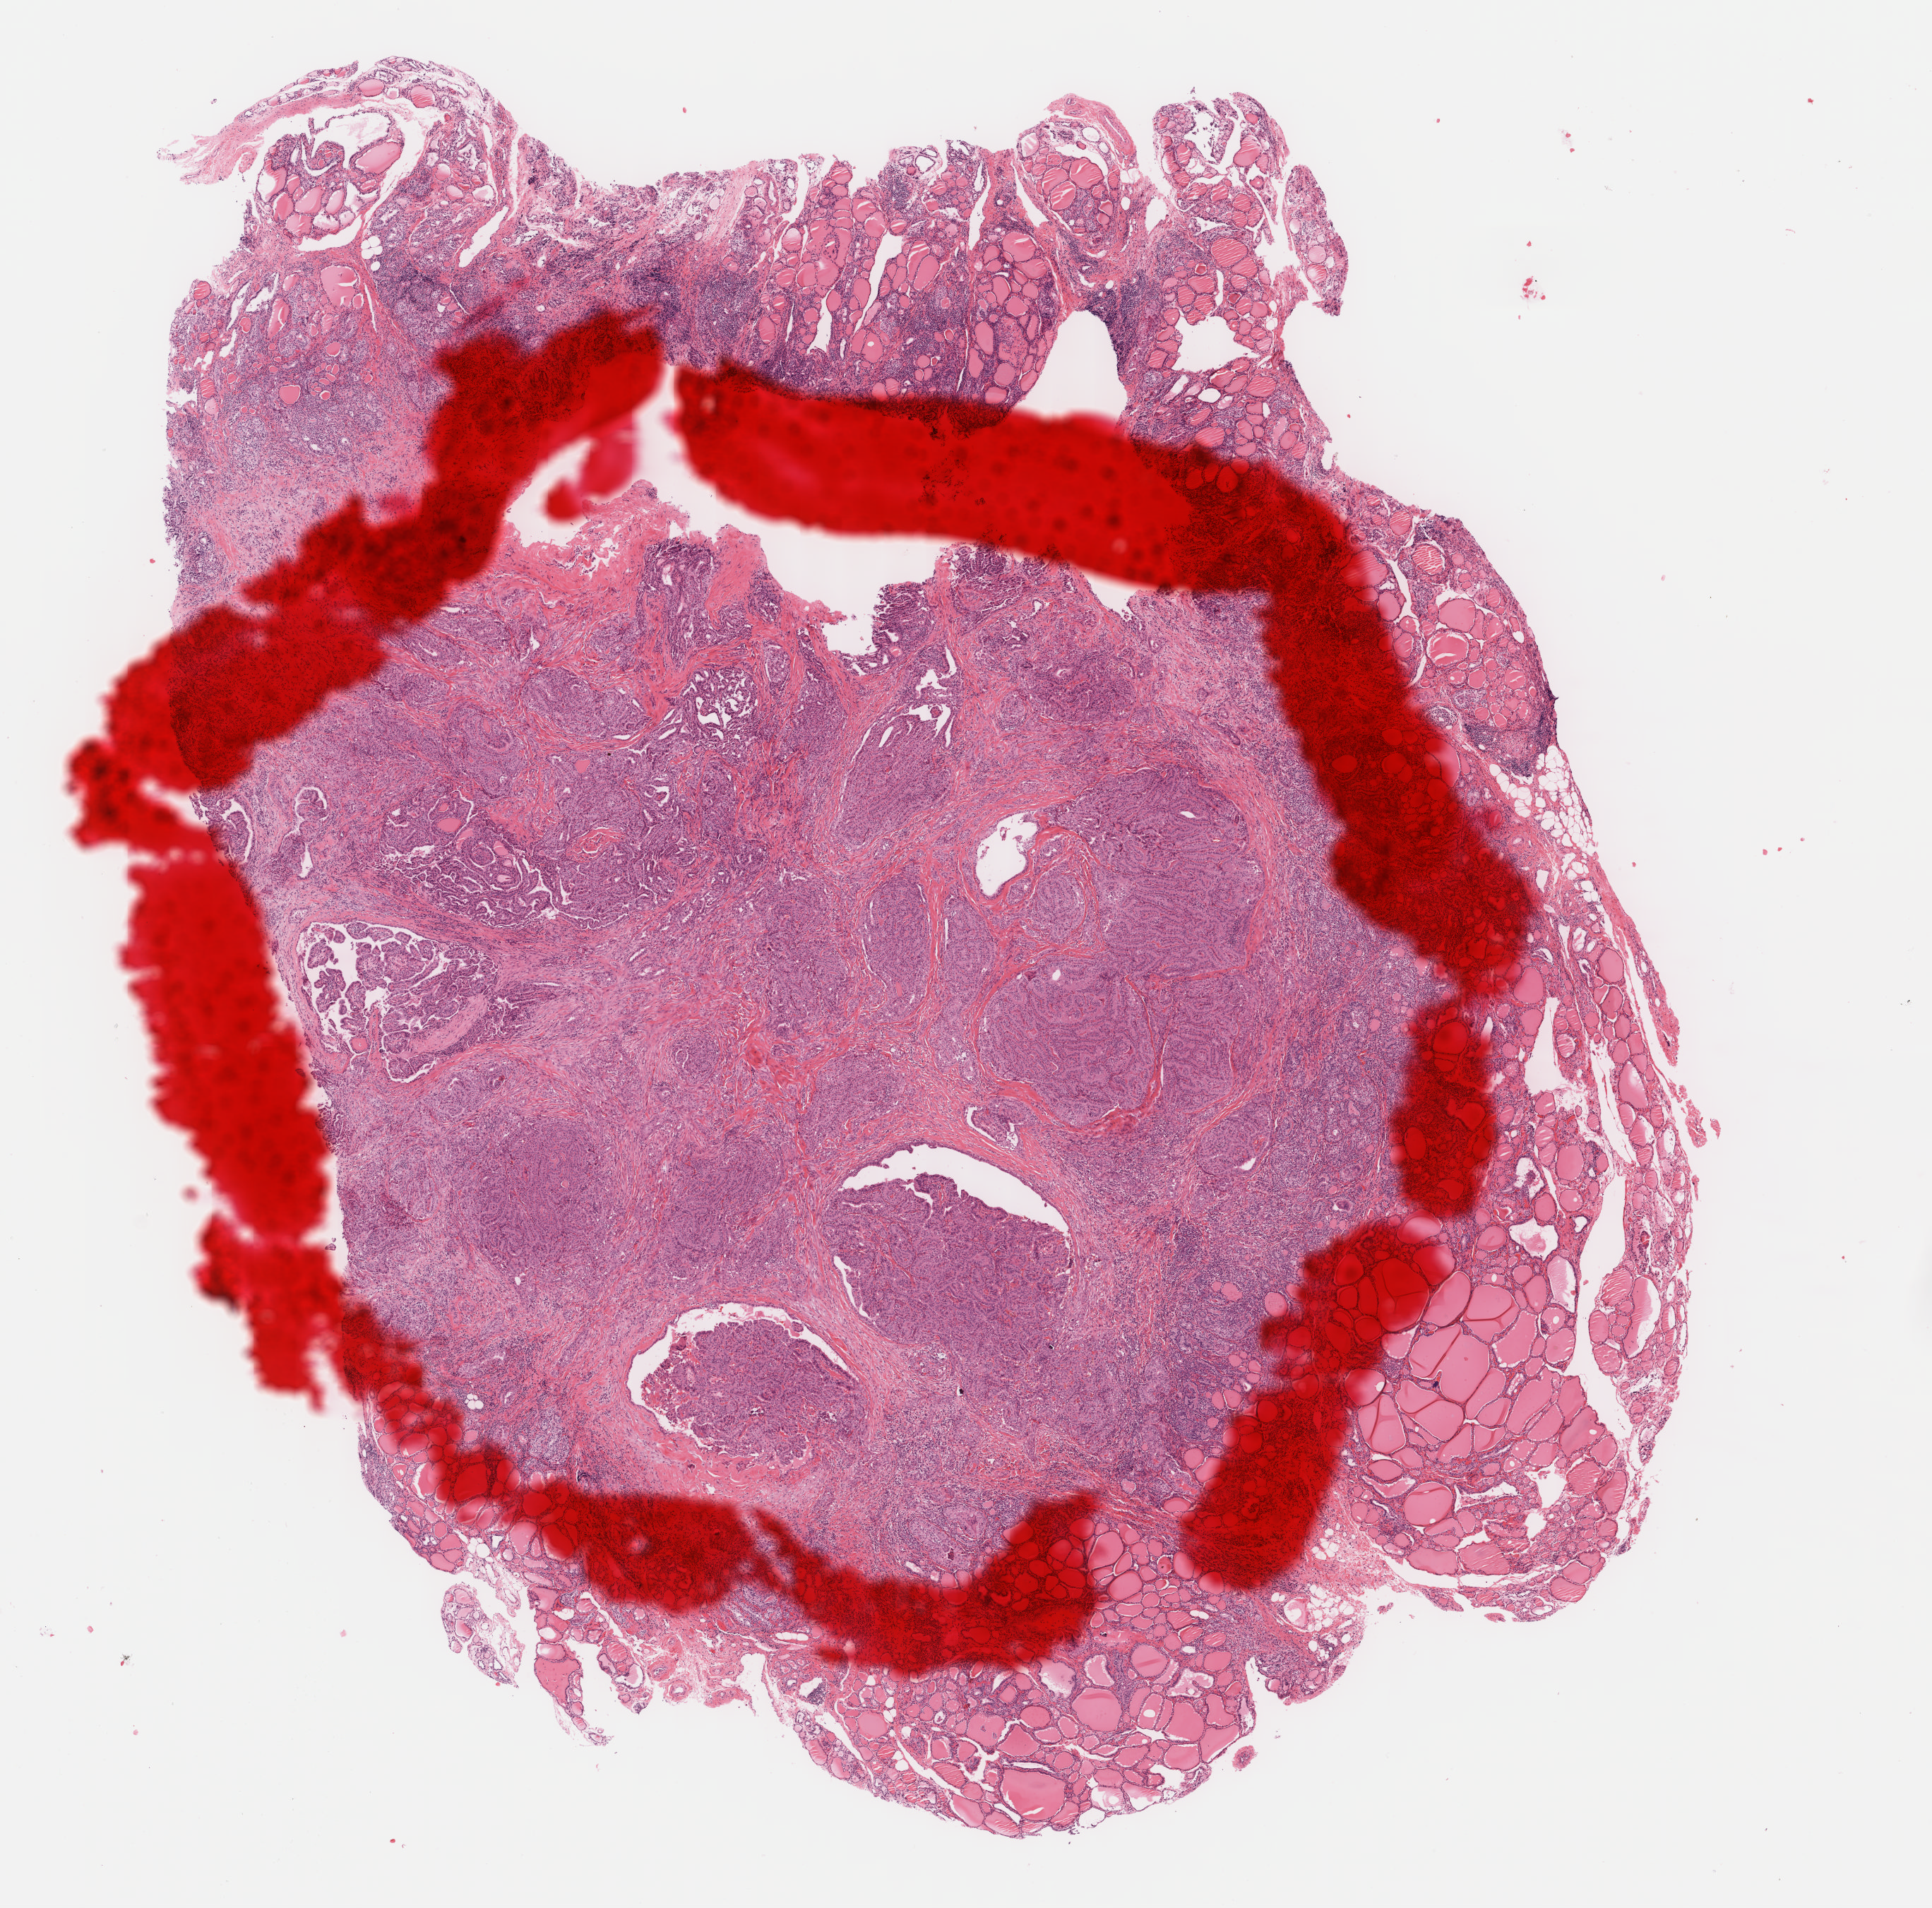
Whole-slide histology image, H&E — shown as a low-resolution overview of the whole scanned area (about 10.9 x 10.7 mm), formalin-fixed paraffin-embedded (FFPE) diagnostic section, thyroid, primary tumour sample. Patient: female, age at initial diagnosis 52 years.
* lymph nodes positive (case pathology): 0 of 12 examined
* laterality: right
* TNM: T1b N0 M0
* histologic diagnosis: Papillary adenocarcinoma, NOS (thyroid gland)
* AJCC pathologic stage: I